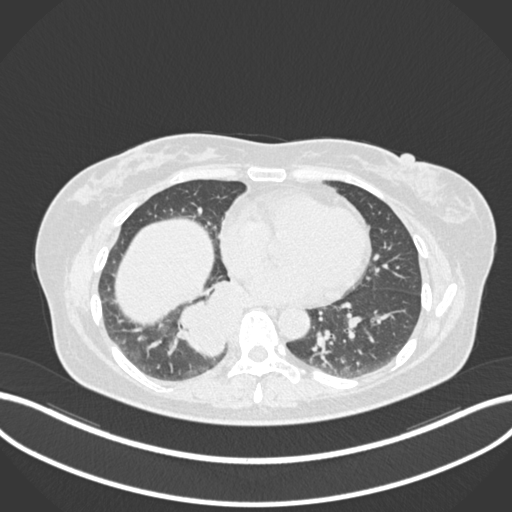
Chest CT, one axial slice. Slice 559 of 677 in the series (ordered by position). 120 kVp. Lung window (W 1500 / L -600 HU). 1 mm slice thickness. 512 × 512 image matrix, field of view 400 × 400 mm. Female patient, age 54 years. Case-level facts recorded for this patient, not image findings: clinical TNM (as recorded): T4 N0 M0.
Annotated regions visible in this slice (bounding box drawn by a radiologist):
- lung tumour (recorded histology: adenocarcinoma): bounding box (x1, y1, x2, y2) in pixels: (175, 274, 241, 359)